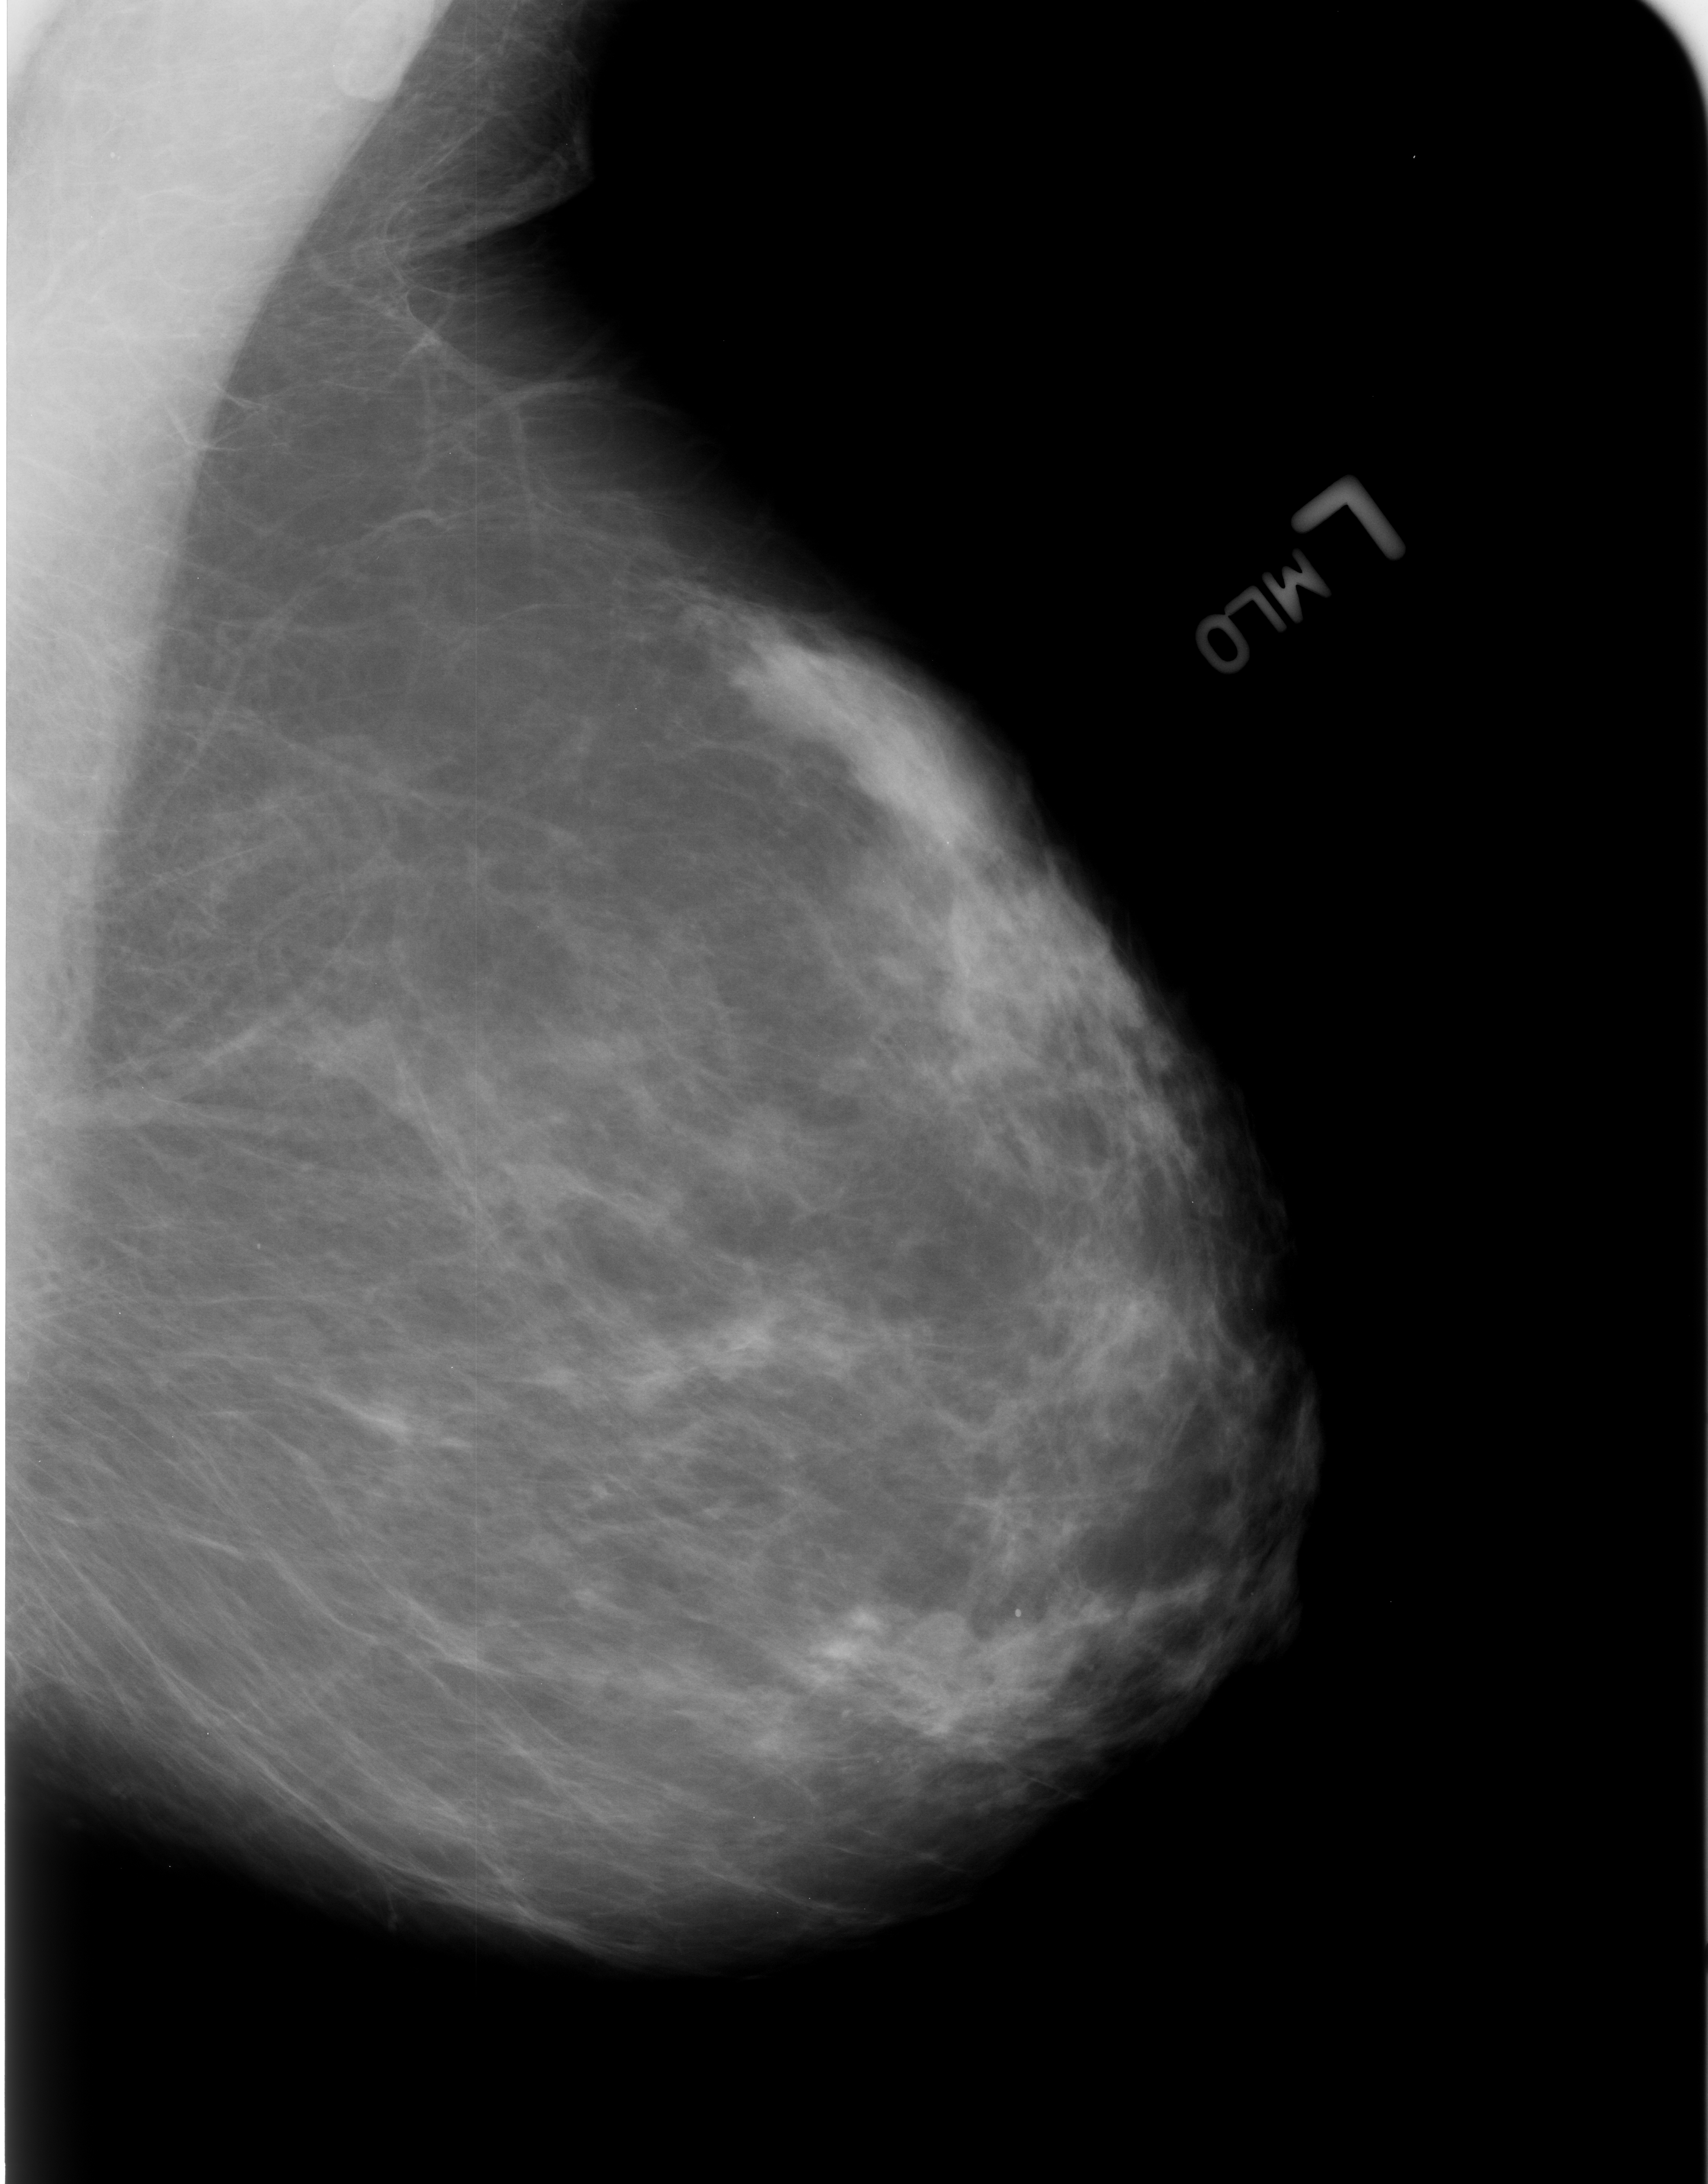
Digitized screen-film mammogram; left breast; mediolateral oblique (MLO) view; BI-RADS breast density category 2 (scale 1–4).
Calcifications, morphology round and regular; BI-RADS assessment category 2; subtlety rating 4 on a 1 (subtle) to 5 (obvious) scale; benign without callback (not worked up further).